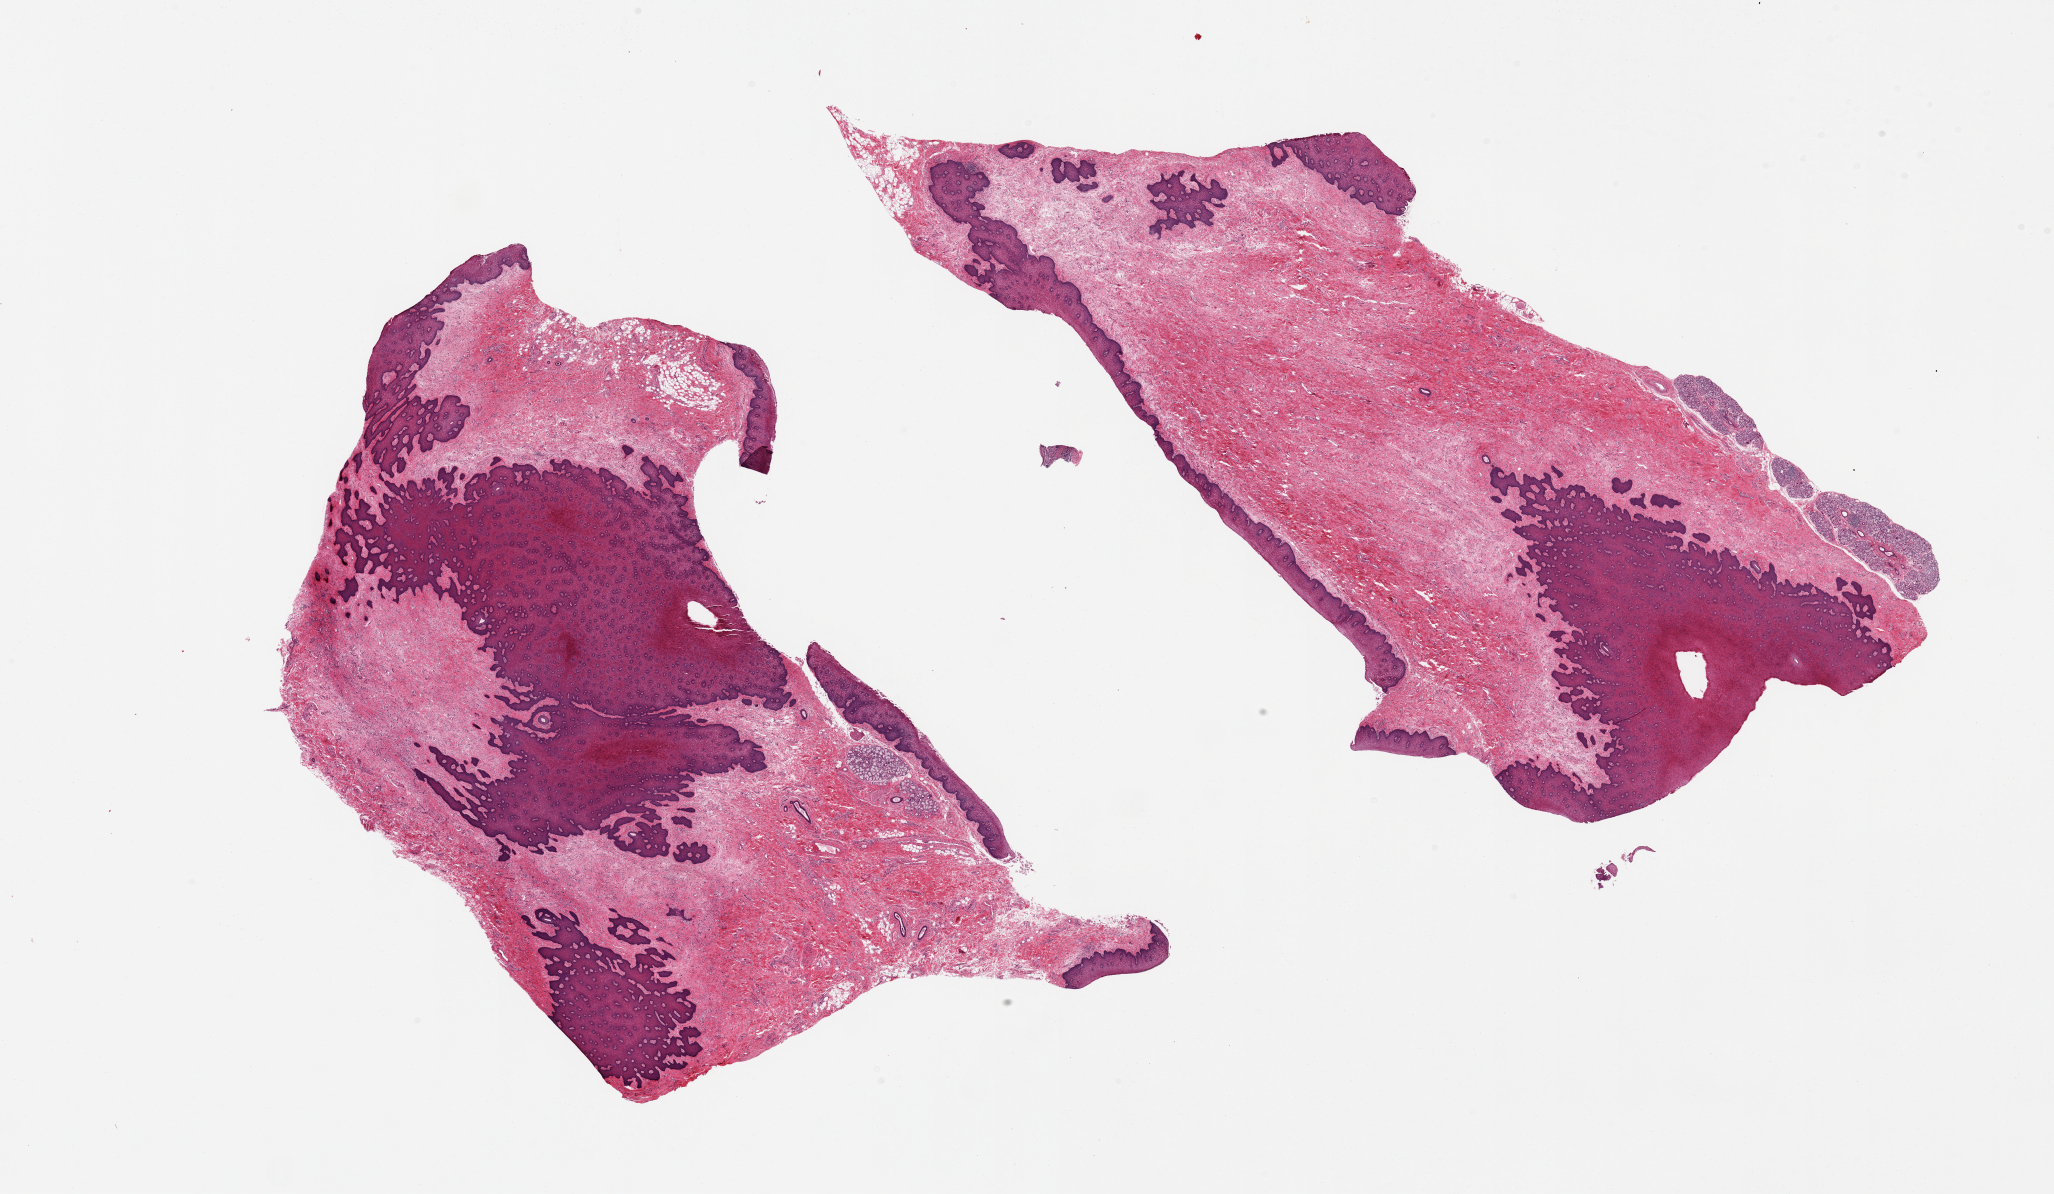
Haematoxylin and eosin whole-slide image, brightfield — whole scanned area (about 32.5 x 18.9 mm, from a 20x scan) shown as a low-resolution overview; PAXgene-fixed, paraffin-embedded tissue; sampled site (target tissue): minor salivary gland; tissue donor sample.
Pathologist's review note for this sample: 2 pieces, 16x10 & 18x9mm; largely squamous mucosa (inner lip) and stroma, minute glands are <5% tissue volume.